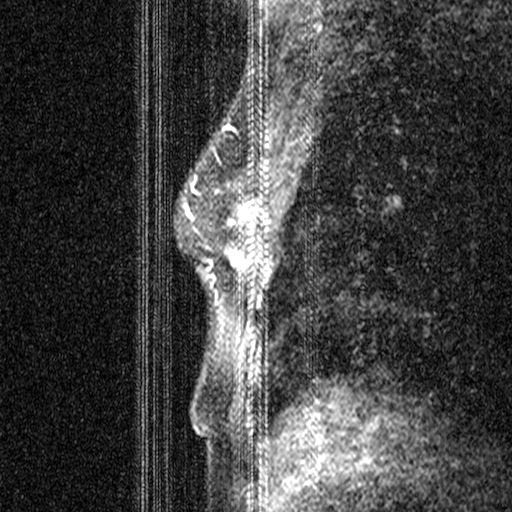
Breast MRI (dynamic contrast-enhanced), one sagittal slice. Slice 22 of 44 in the series (ordered by position). Dynamic contrast-enhanced study with each time point stored as its own series, time point 2 of 3 at this slice position (early post-contrast, ordered by acquisition time). 1.5 T. TE 4.5 ms, TR 11 ms. 3 mm slice thickness. 512 × 512 image matrix. Female patient, age 44 years. Case-level facts recorded for this patient, not image findings: setting: breast cancer imaged before/during neoadjuvant chemotherapy; receptor status: HR-positive, HER2-negative.
Outlined on this slice (semi-automatic segmentation, software-assisted and operator-edited):
- analysis volume of interest (the breast-tissue region the enhancement analysis was run in; not a lesion): box from (x=206, y=164) to (x=252, y=299) px
- tumour enhancement mask (voxels above the 90 % enhancement threshold inside the analysis volume of interest): (x=206, y=164)–(x=252, y=270)